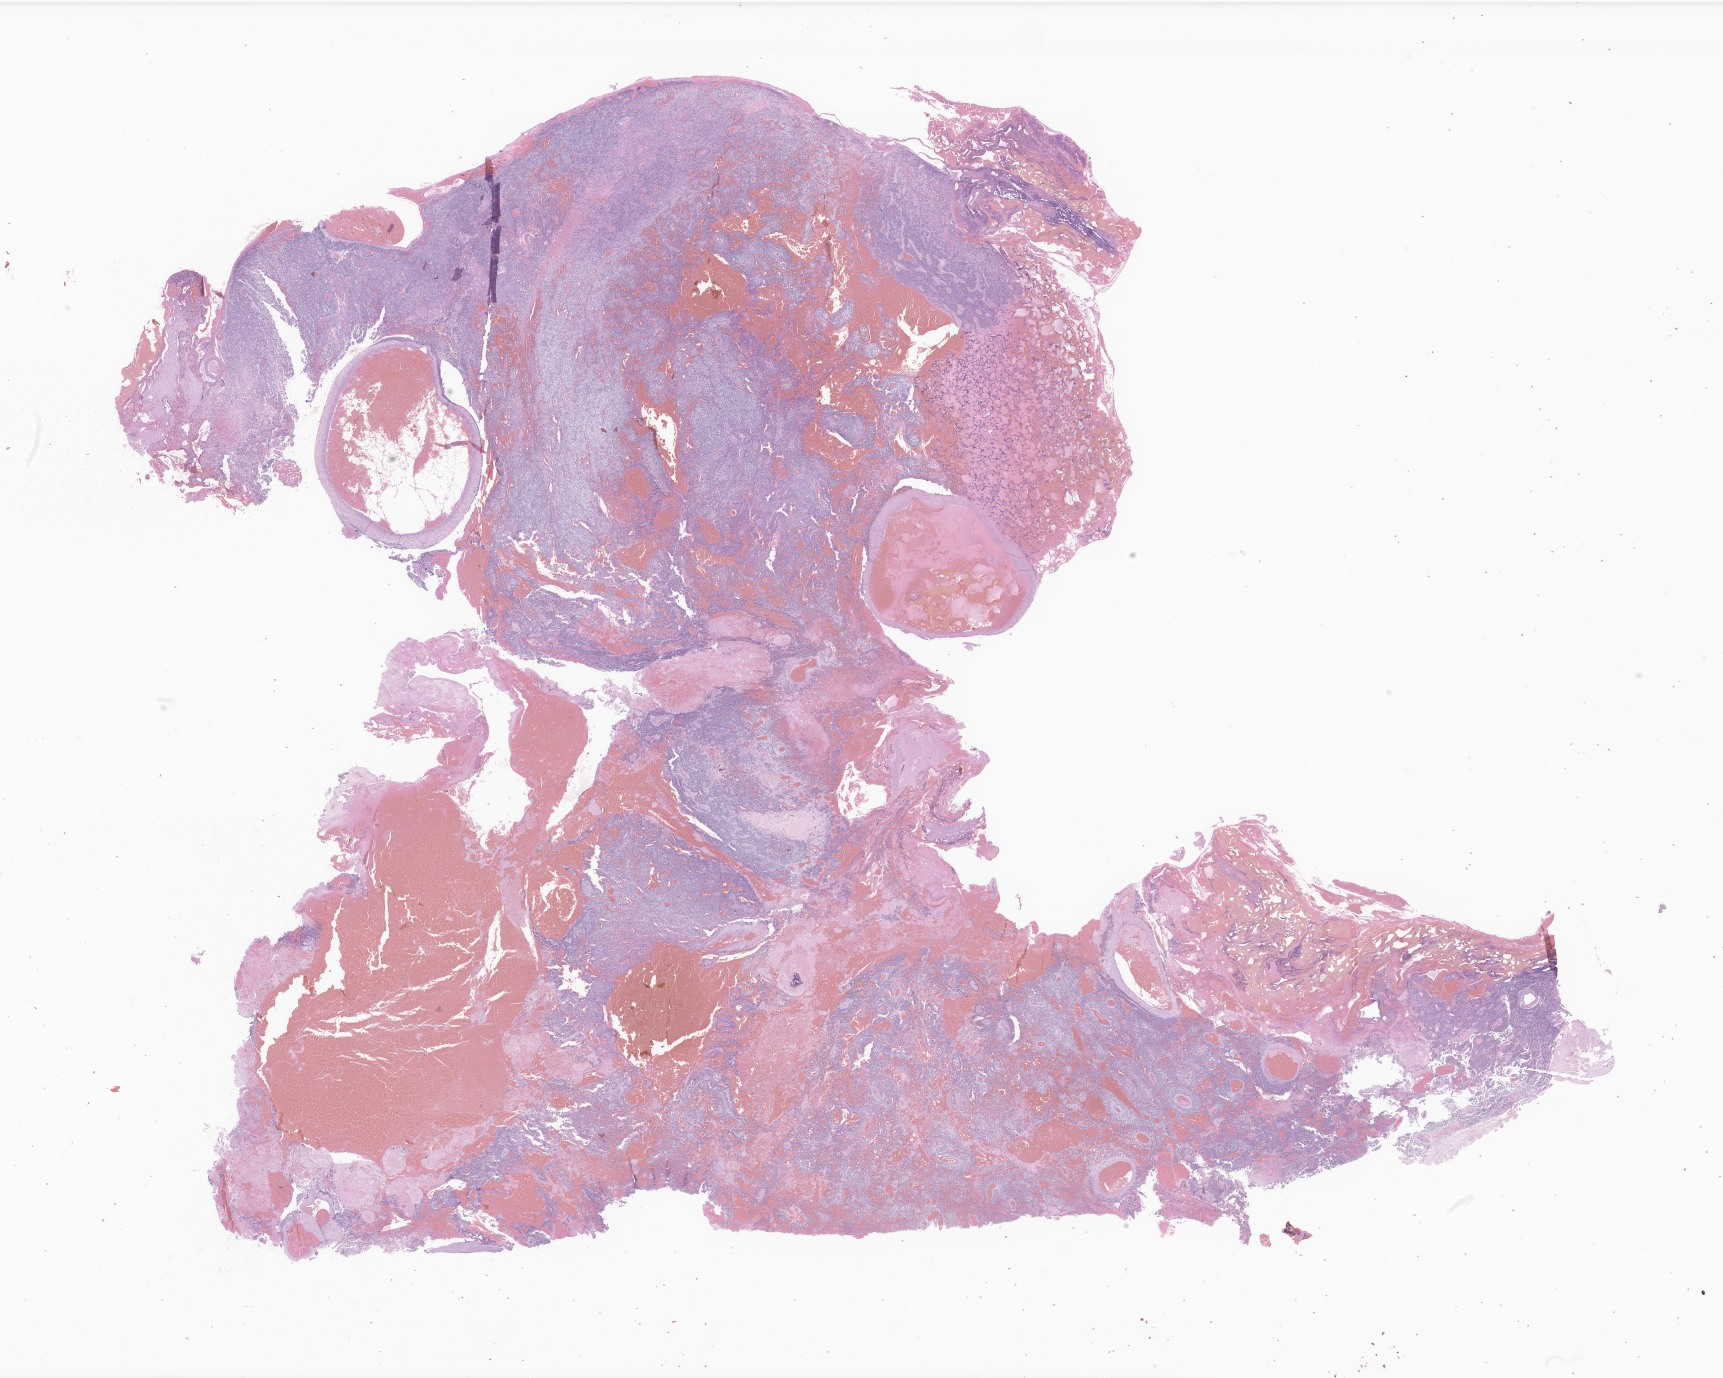
Haematoxylin and eosin whole-slide image of tumor tissue from the brain — a low-resolution overview of the entire scanned area, about 29.1 x 23.2 mm; FFPE section. Female patient, age 51 months (4 years 3 months).
Diagnosis: Neoplasm, malignant.